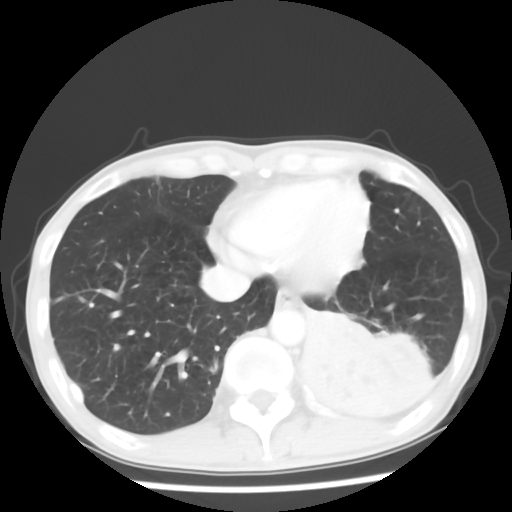
Chest CT, one axial slice; slice 15 of 64 in the series (ordered by position); lung window (W 1500 / L -600 HU); 512 × 512 image matrix. Male patient, age 68 years. Case-level facts recorded for this patient, not image findings: clinical TNM (as recorded): T4 N0 M0.
Annotated regions visible in this slice (bounding box drawn by a radiologist):
- lung tumour (recorded histology: squamous cell carcinoma): bounding box <300,316,417,432> (left, top, right, bottom; pixels)